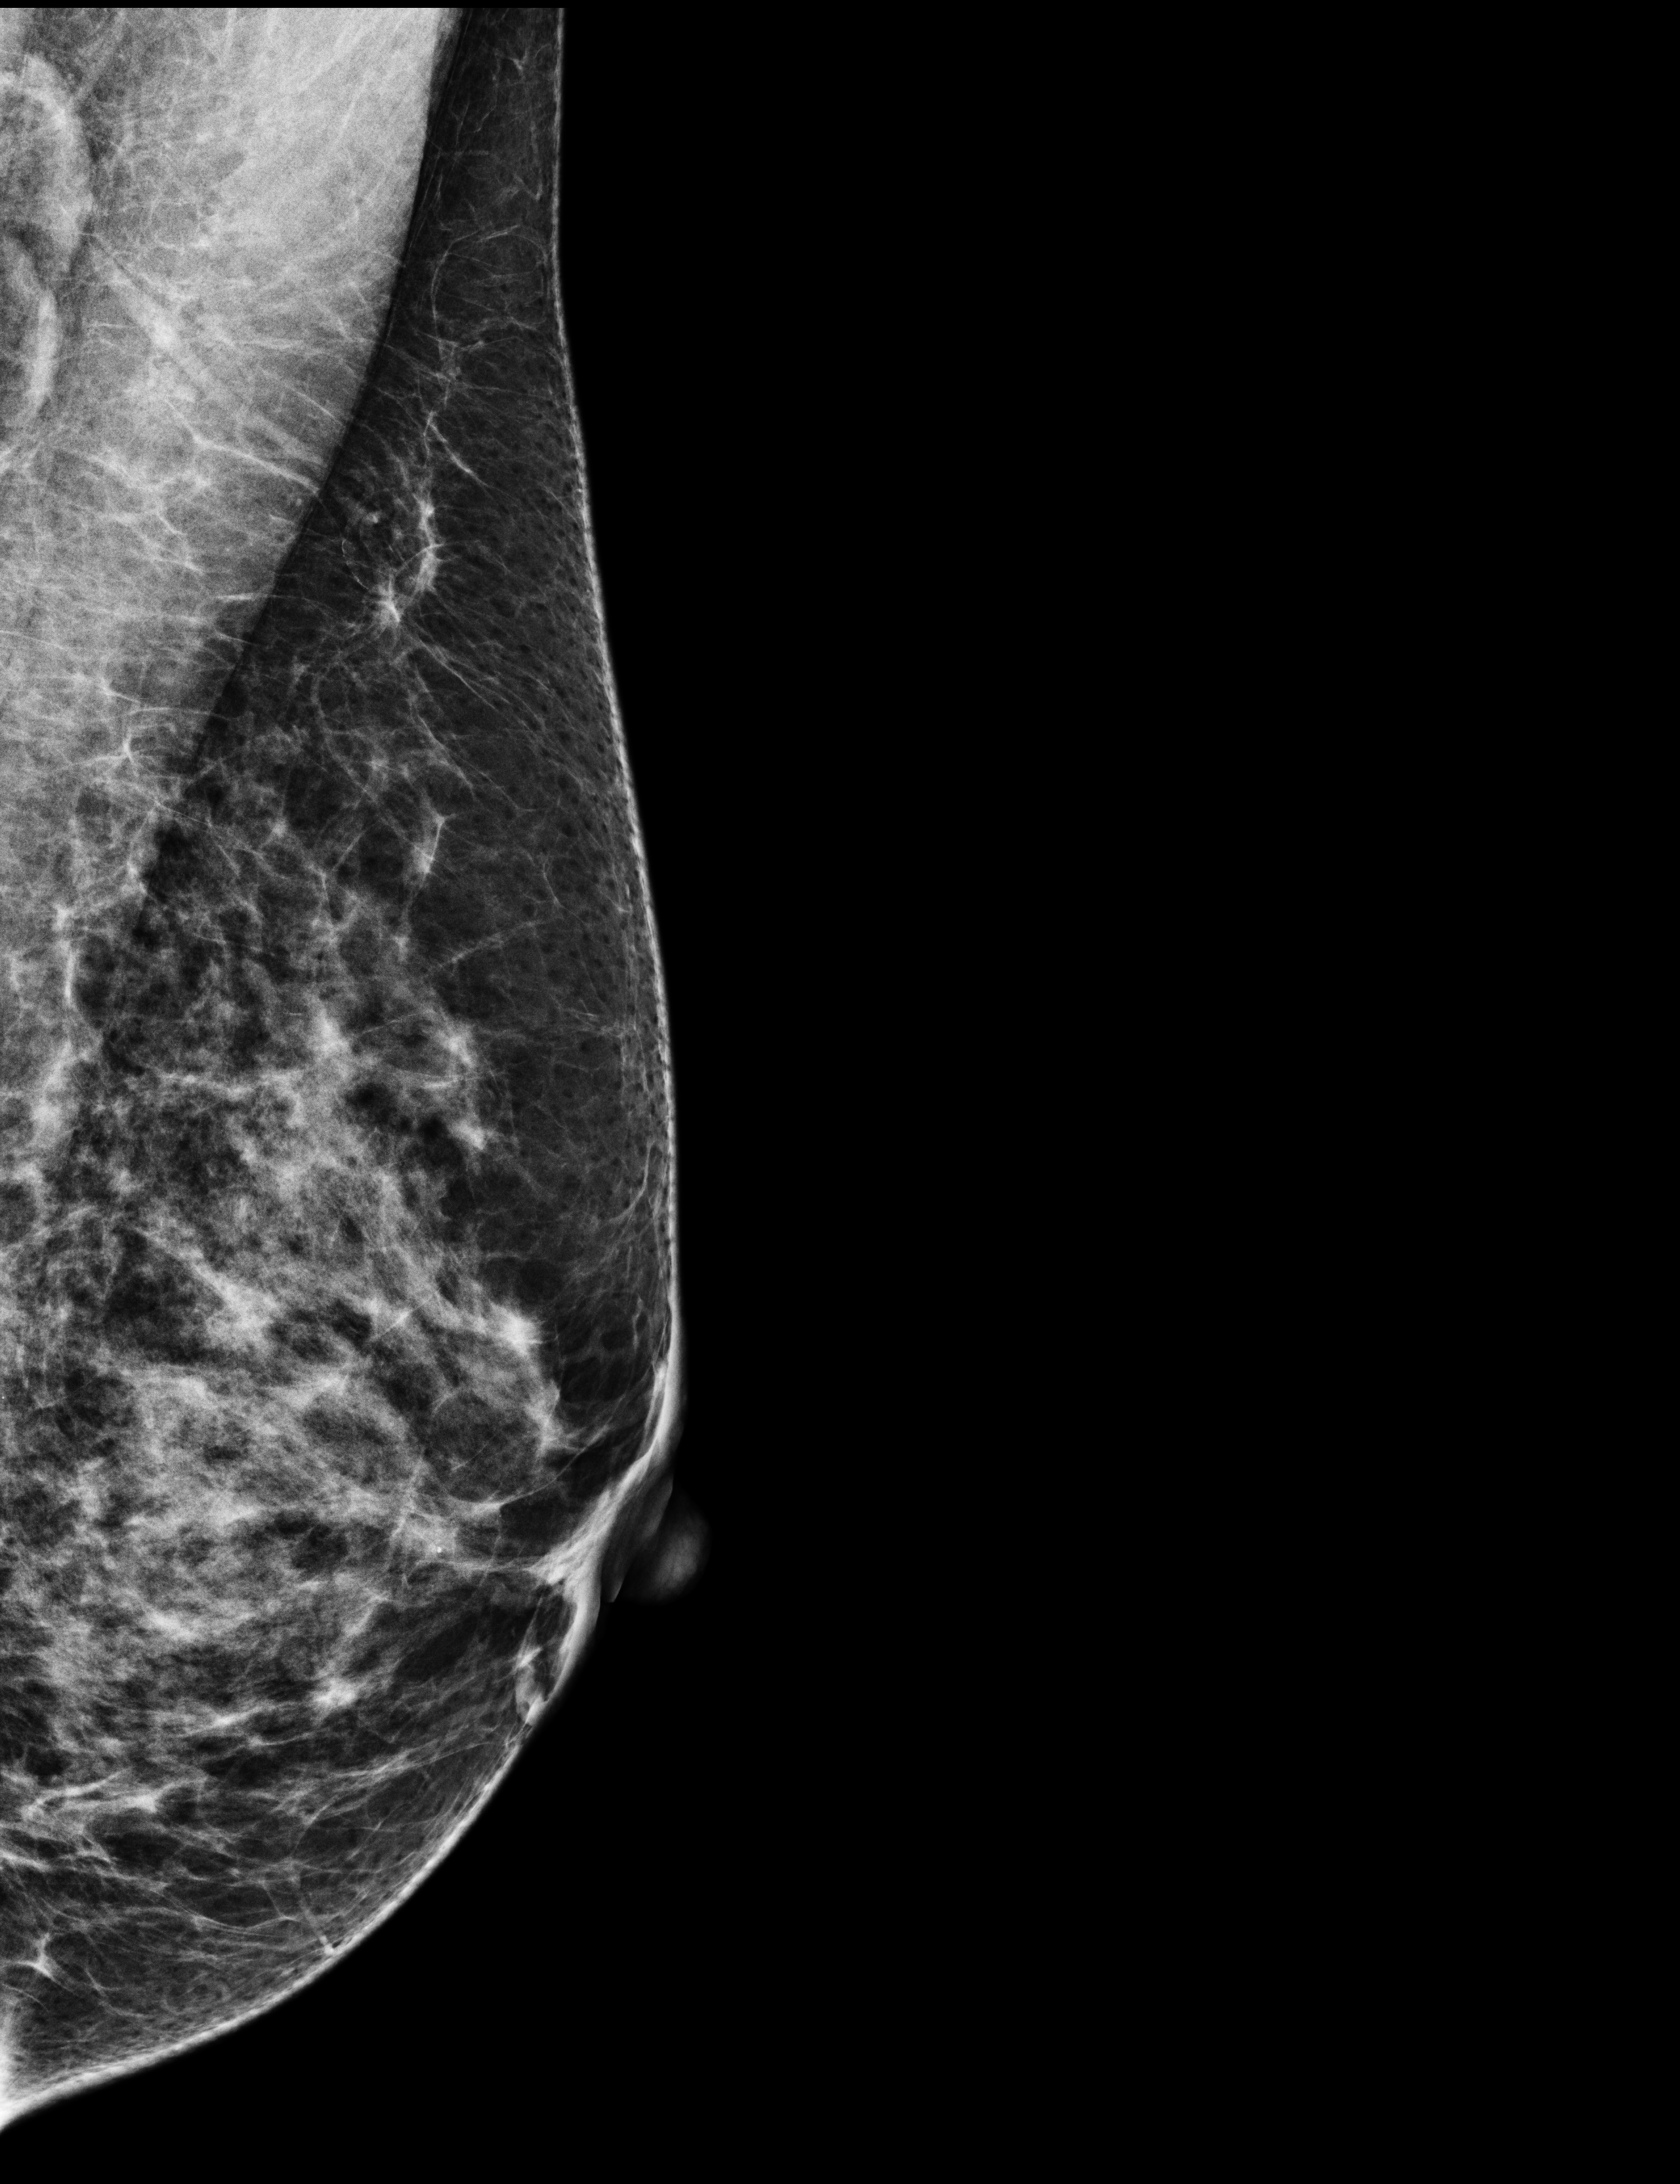
Annual screening mammography examination; compressed breast thickness 50 mm; system: Selenia Dimensions. Female patient, age 55 years.
Image type: full-field digital mammogram. Breast: left. Projection: medio-lateral oblique projection.